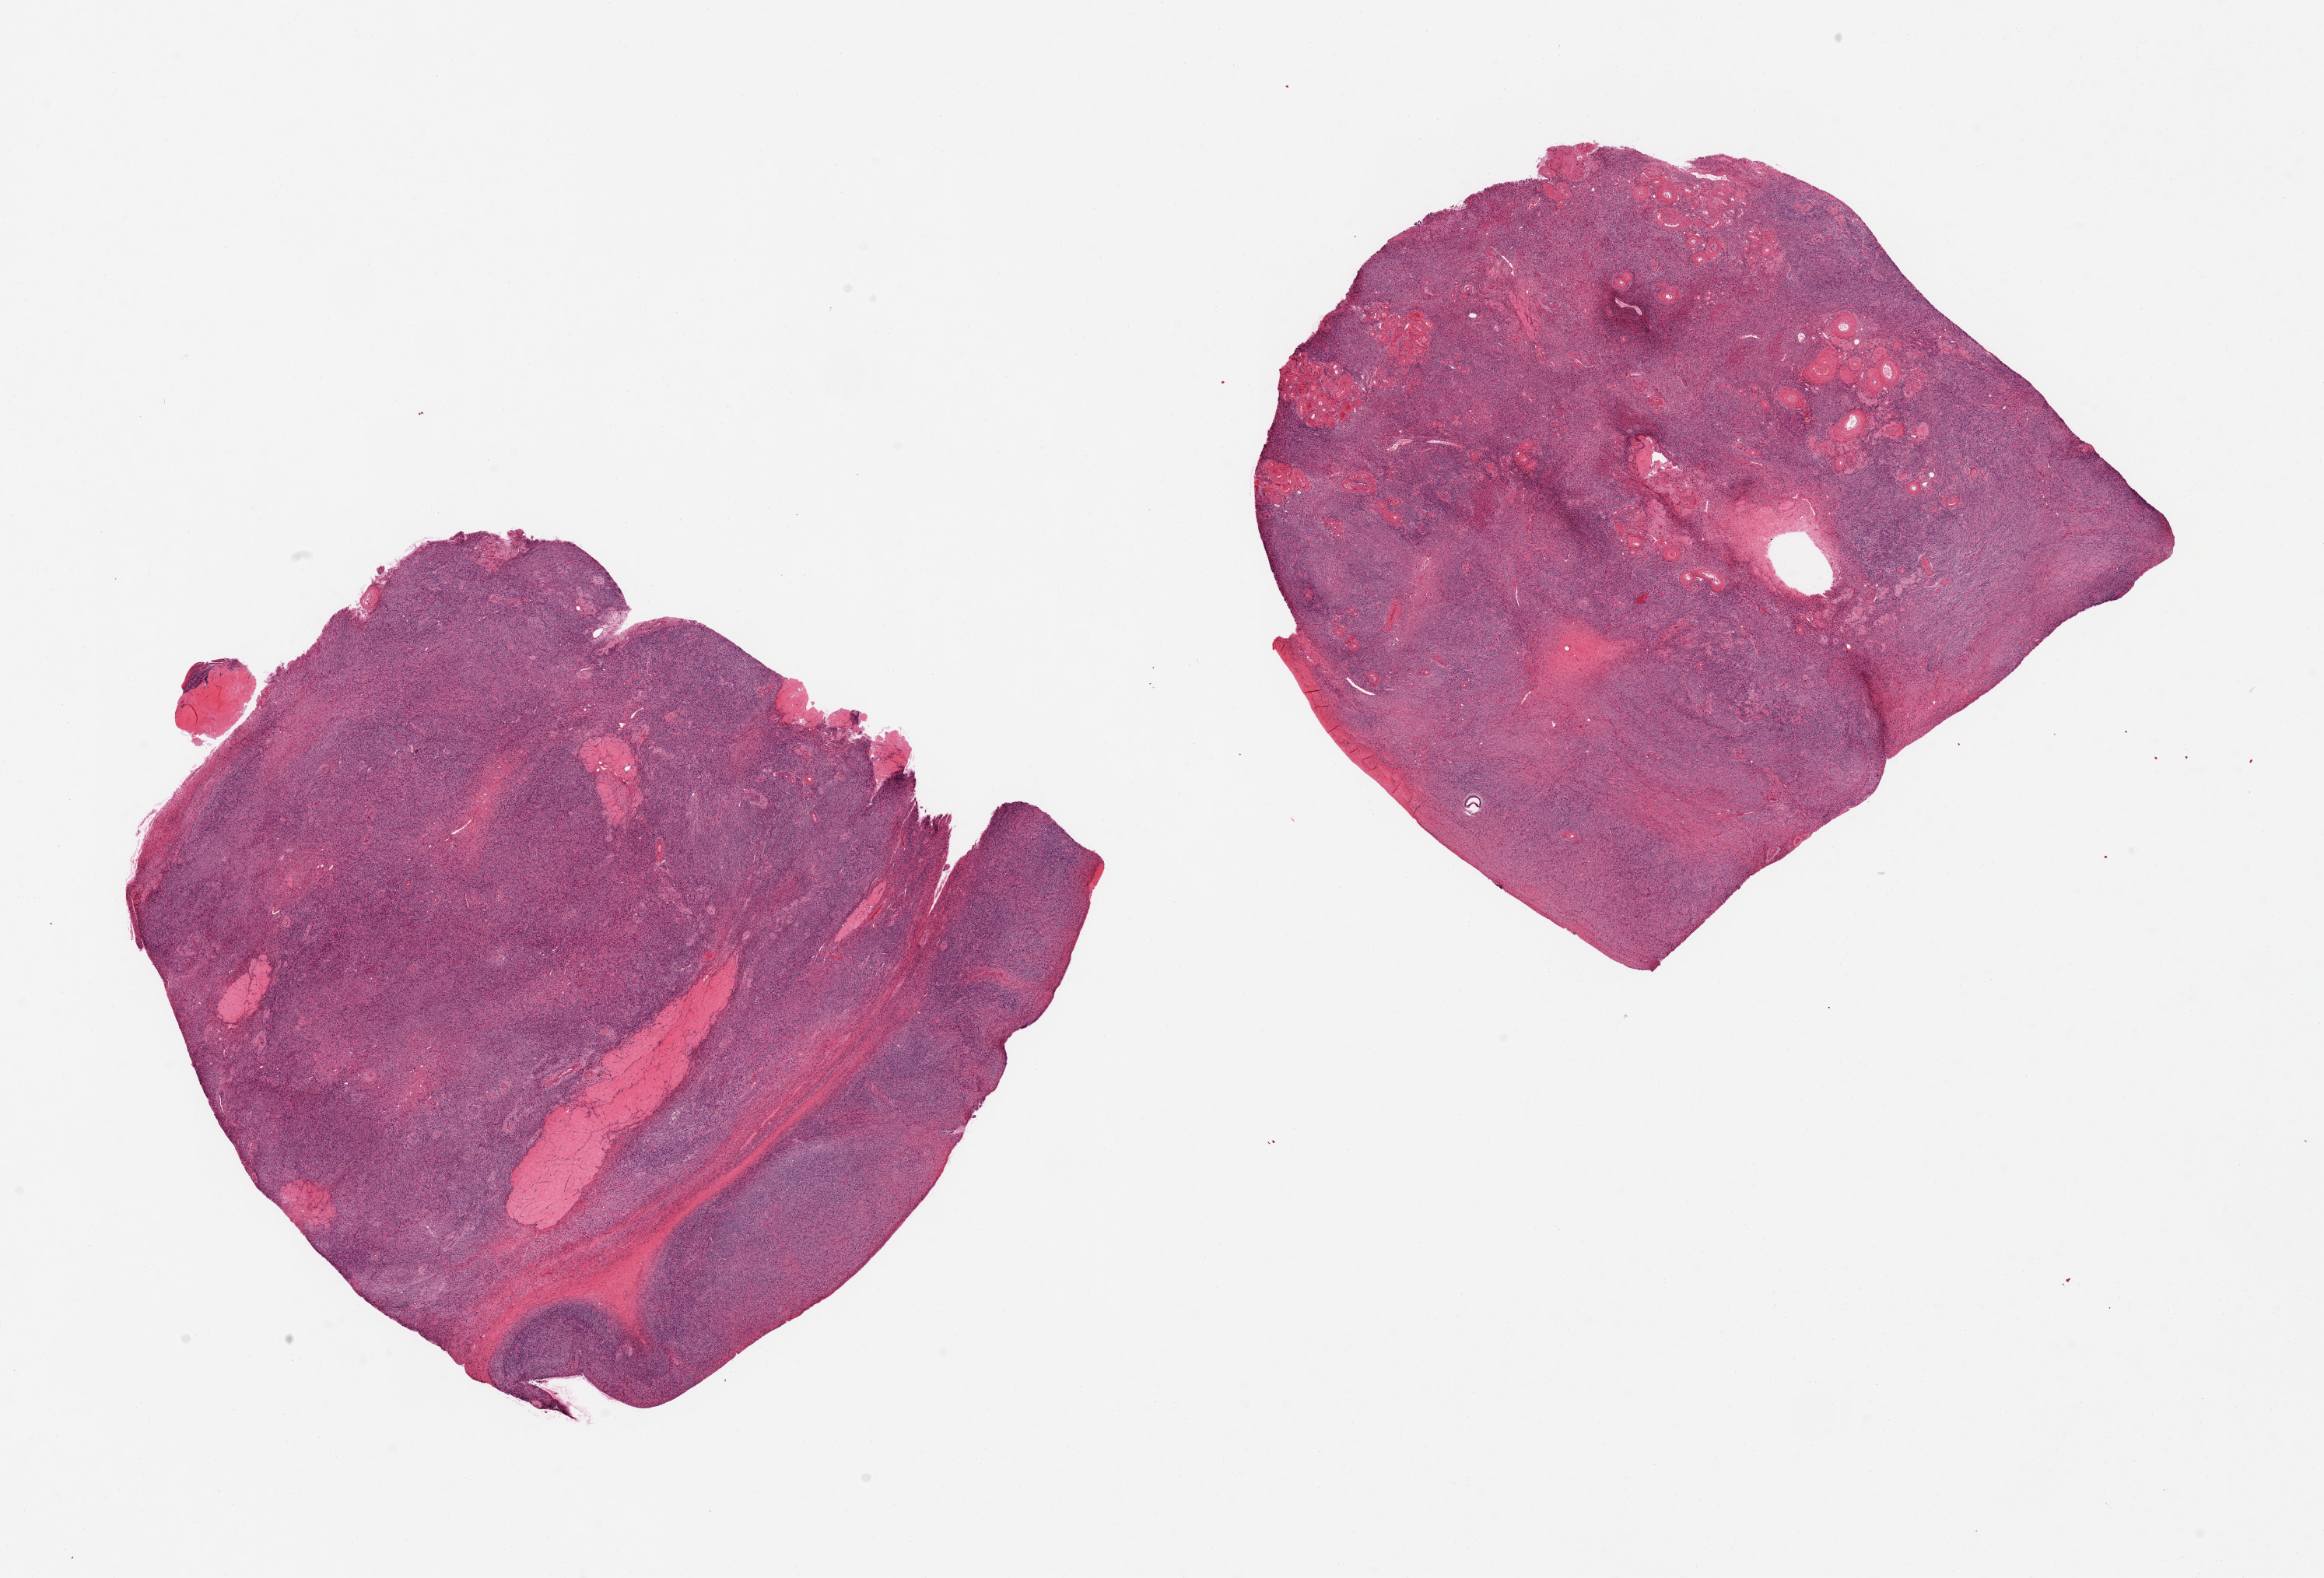
Whole-slide image, hematoxylin and eosin (H&E) stain, brightfield, low-resolution overview of the scanned area, about 23.6 x 16.0 mm, PAXgene-fixed, paraffin-embedded tissue, sampled site (target tissue): ovary, donor tissue sample. Donor: female.
Review note (as recorded): 2 pieces, typical post menopausal atrophy.